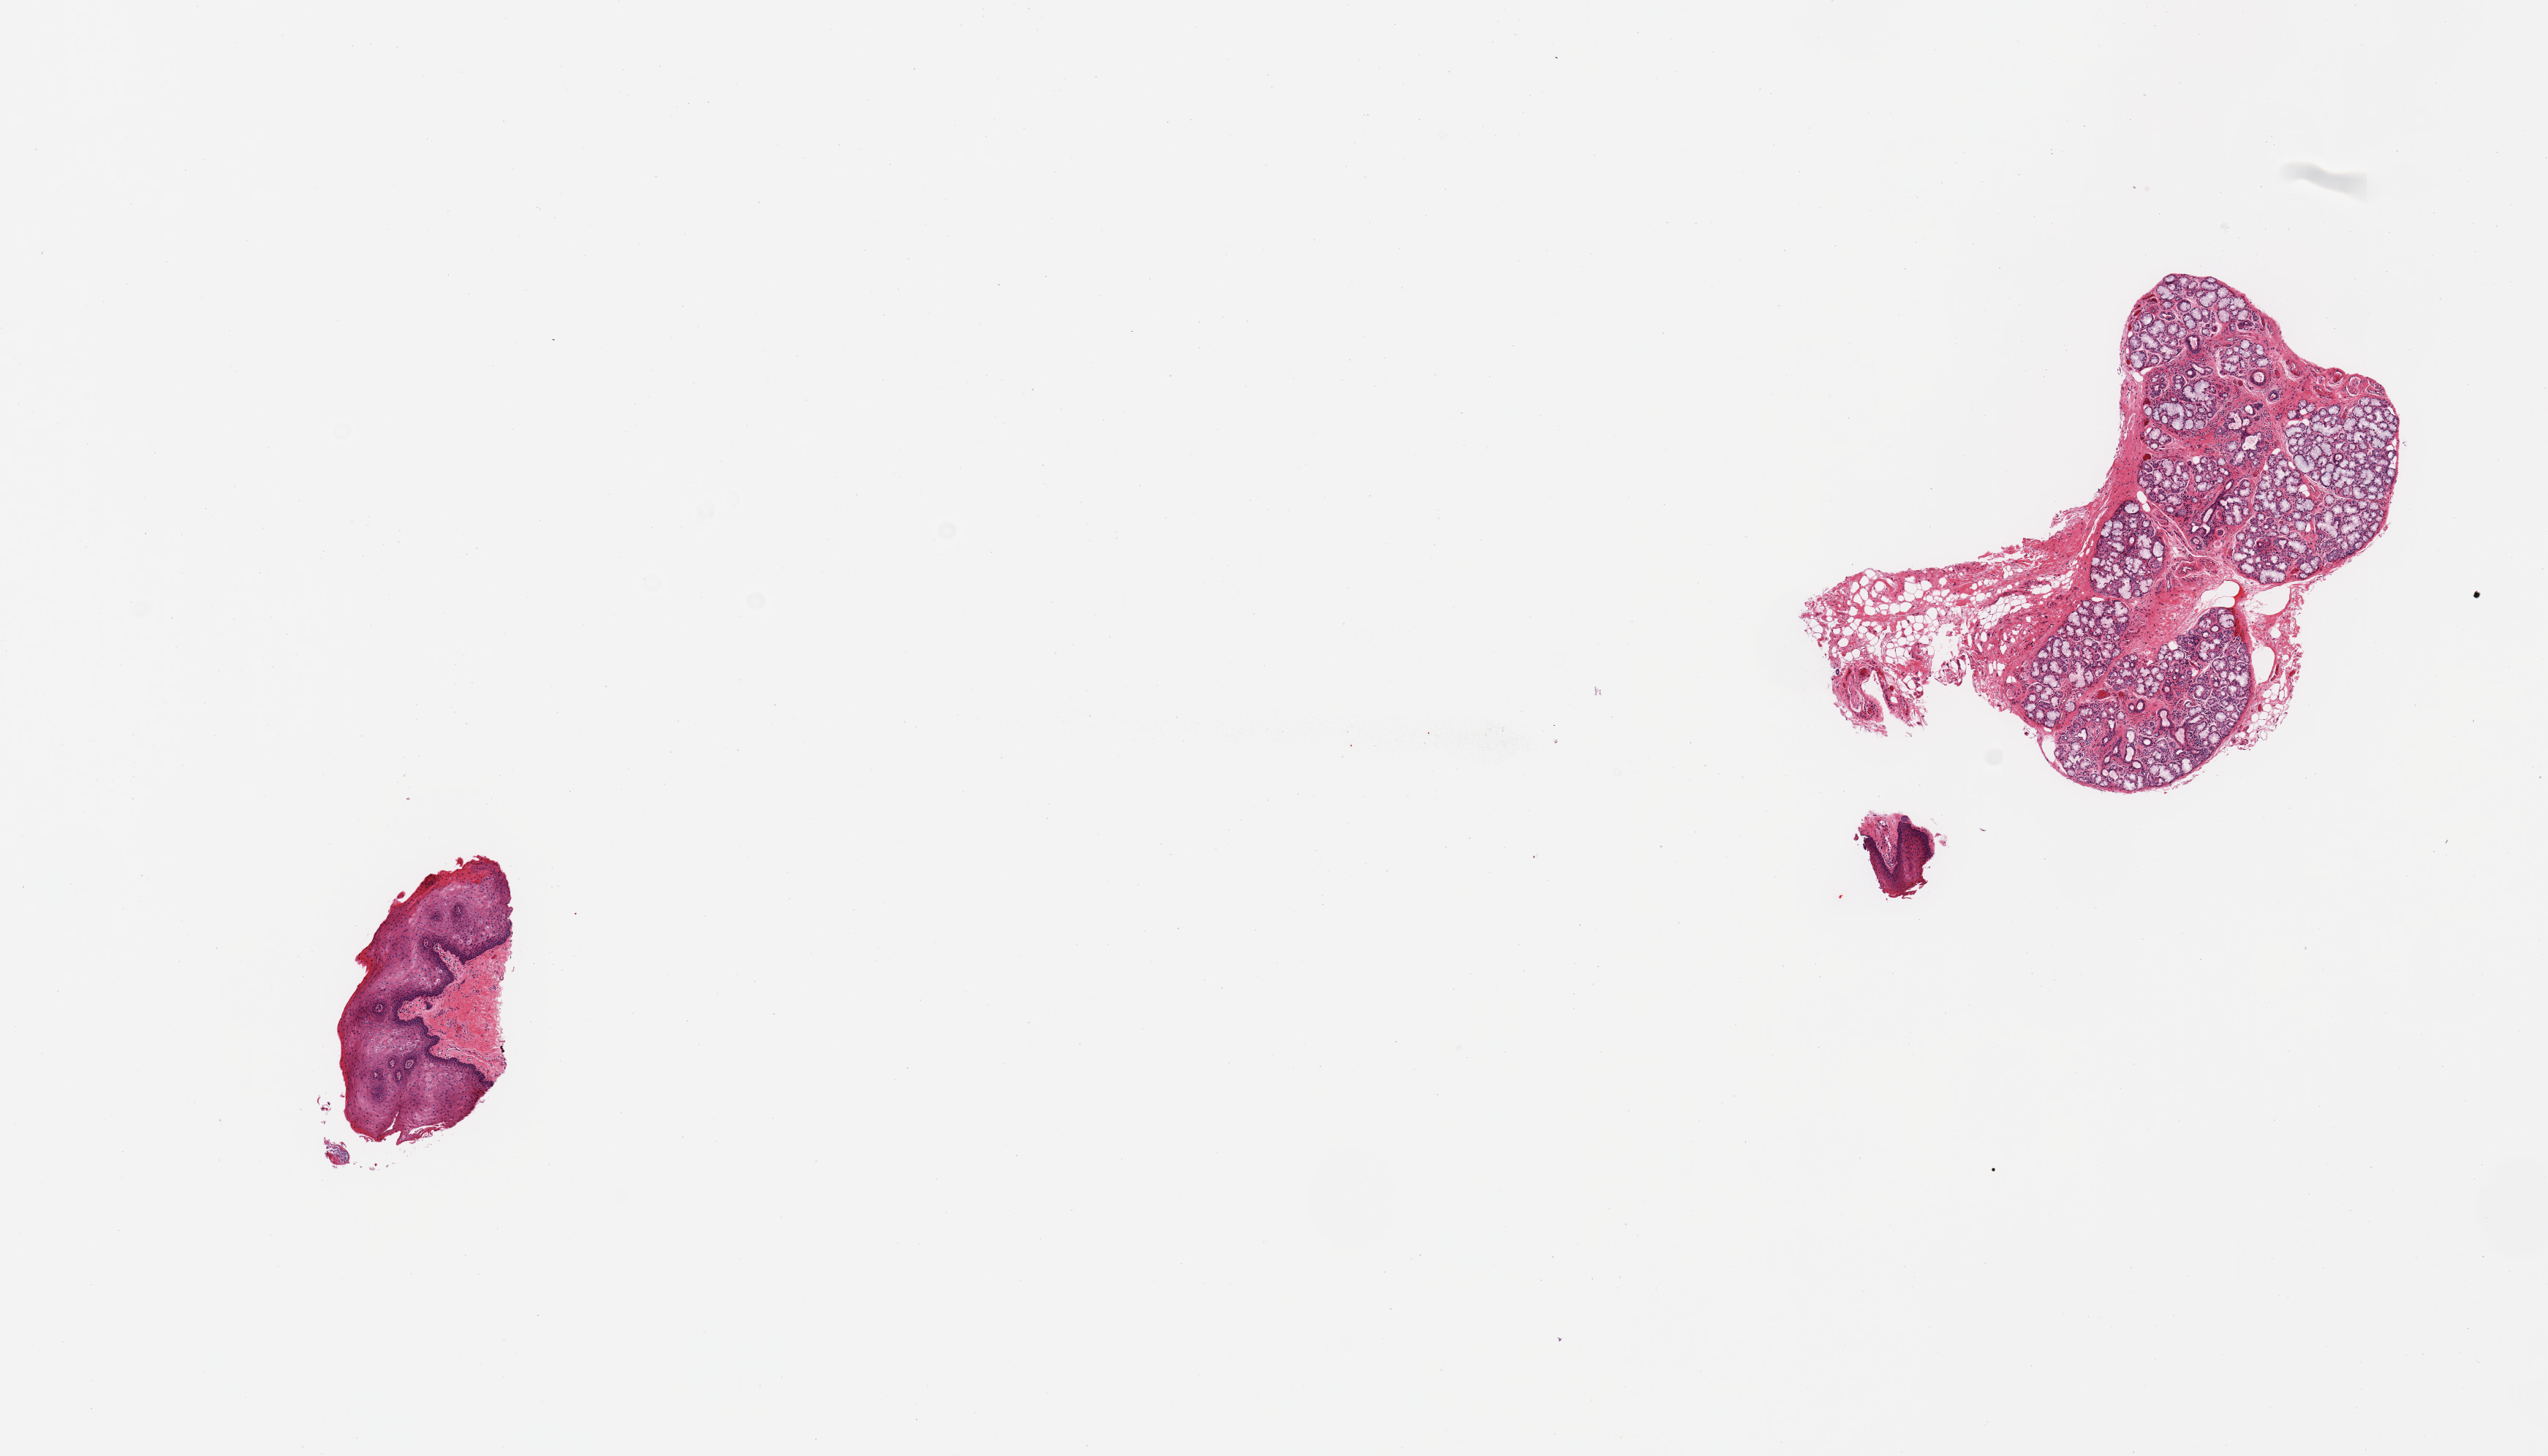
Hematoxylin and eosin (H&E) whole-slide image, a low-resolution overview of the entire scanned area, about 13.8 x 7.9 mm (acquisition: 20x scan). PAXgene-fixed, paraffin-embedded tissue. Section of minor salivary gland (target tissue). Tissue donor sample. Donor sex: male.
Pathologist's review note for this sample: 2 pieces; 1 piece is portion of lip, 2nd is salivary gland elements with attachment of fat (~20%).